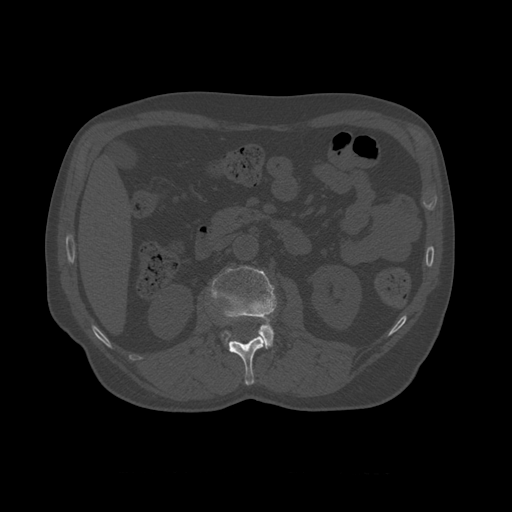
CT including the spine, one axial slice. Slice 344 of 450 in the series (ordered by position). Reconstruction kernel STANDARD. 120 kVp. Bone window (W 1800 / L 400 HU). 512 × 512 image matrix, field of view 405 × 405 mm. Patient age 75 years. Case-level facts recorded for this patient, not image findings: primary cancer: prostate.
Annotated regions visible in this slice (semi-automatic segmentation, software-assisted and operator-edited):
- L1 vertebra: bounding box (x1, y1, x2, y2) in pixels: (228, 336, 266, 386)
- L2 vertebra: (209, 266, 277, 349)